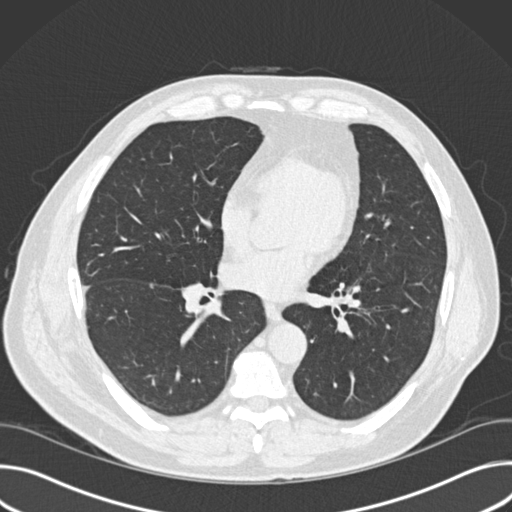
Low-dose screening chest CT, one axial slice. Position 77 of 157 along the scan axis. Reconstruction kernel B30f. 120 kVp. Lung window (W 1500 / L -600 HU). 2 mm slice thickness. 512 × 512 image matrix, field of view 380 × 380 mm.
Structures marked on this image (expert manual segmentation):
- lesion 1 (tumor, upper lobe of right lung): box from (x=85, y=286) to (x=88, y=290) px